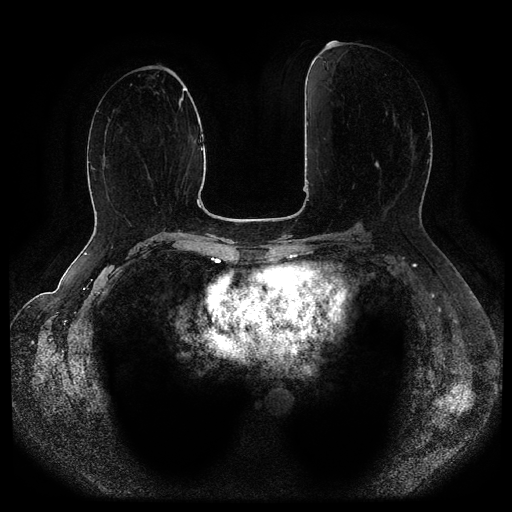
Breast MRI (dynamic contrast-enhanced, multi-phase), one axial slice; position 46 of 116 along the scan axis; dynamic contrast-enhanced series, time point 2 of 5 at this slice position (early post-contrast); 1.5 T; TE 2.6 ms, TR 5.3 ms; 512 × 512 image matrix, field of view 360 × 360 mm. Patient: female, 55 years.
Annotated regions visible in this slice (semi-automatic segmentation, software-assisted and operator-edited):
- breast lesion (labelled benign in the annotation): bounding box (x1, y1, x2, y2) in pixels: (375, 161, 379, 168)